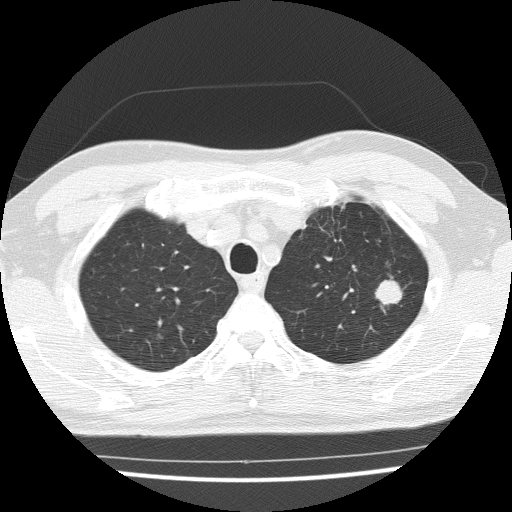
Low-dose screening chest CT, axial slice, third screening round (two years after baseline), lung window (W 1500 / L -600 HU), lung (sharp) reconstruction kernel (FC51), 120 kVp, slice 34 of 154 in the series, 512 × 512 image matrix. Male, age 65 years at enrolment. Current smoker at enrolment.
• Lesion marked by an expert reader, bounding box [x1, y1, x2, y2] px = [357, 272, 410, 318].
• Screening reader's record for this exam (one nodule recorded; not confirmed to be the boxed lesion): non-calcified nodule or mass ≥4 mm, left upper lobe, 16 × 15 mm, poorly defined margins, soft tissue attenuation, pre-existing on the prior screen: yes; interval growth: yes.
• Official screen result: positive, other.
• Lung cancer was diagnosed 42 days after this screen: squamous cell carcinoma, NOS, left upper lobe, moderately differentiated (G2), stage IA (AJCC 6th edition), 25 mm at pathology.